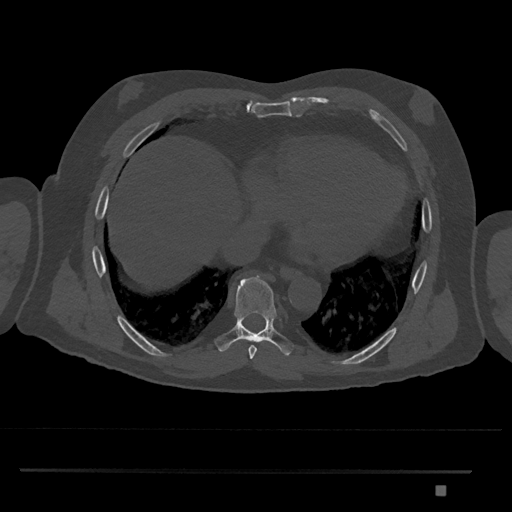
CT including the spine, one axial slice. Slice 1118 of 1134 in the series (ordered by position). Reconstruction kernel Br40s/3. 120 kVp. Bone window (W 1800 / L 400 HU). 0.5 mm slice thickness. 512 × 512 image matrix, field of view 429 × 429 mm. Patient: male, 65 years. From the clinical record (not read from this slice): primary cancer: prostate.
Structures marked on this image (semi-automatic segmentation, software-assisted and operator-edited):
- T8 vertebra: bounding box [x1, y1, x2, y2] px = [214, 275, 294, 356]